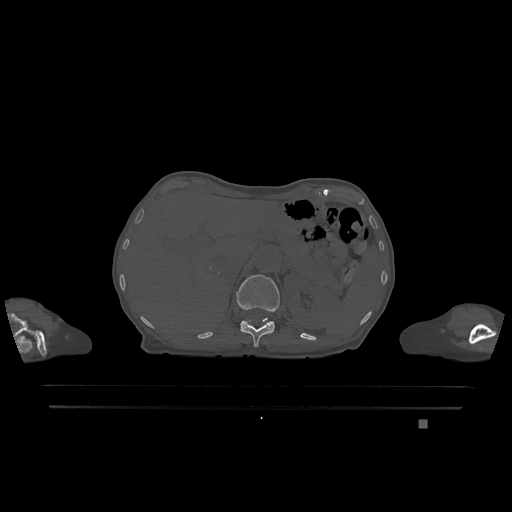
CT including the spine, one axial slice. Slice 505 of 1317 in the series (ordered by position). Bone window (W 1800 / L 400 HU). 0.5 mm slice thickness. 512 × 512 image matrix, field of view 500 × 500 mm. Female patient, age 74 years. From the clinical record (not read from this slice): primary cancer: lung; vertebrae with lytic lesions (as recorded): T1, T4, T5, T6, L4, L5.
Structures marked on this image (semi-automatically segmented with operator editing):
- L1 vertebra: bounding box [x1, y1, x2, y2] px = [237, 274, 280, 333]
- T12 vertebra: [242, 318, 271, 347]